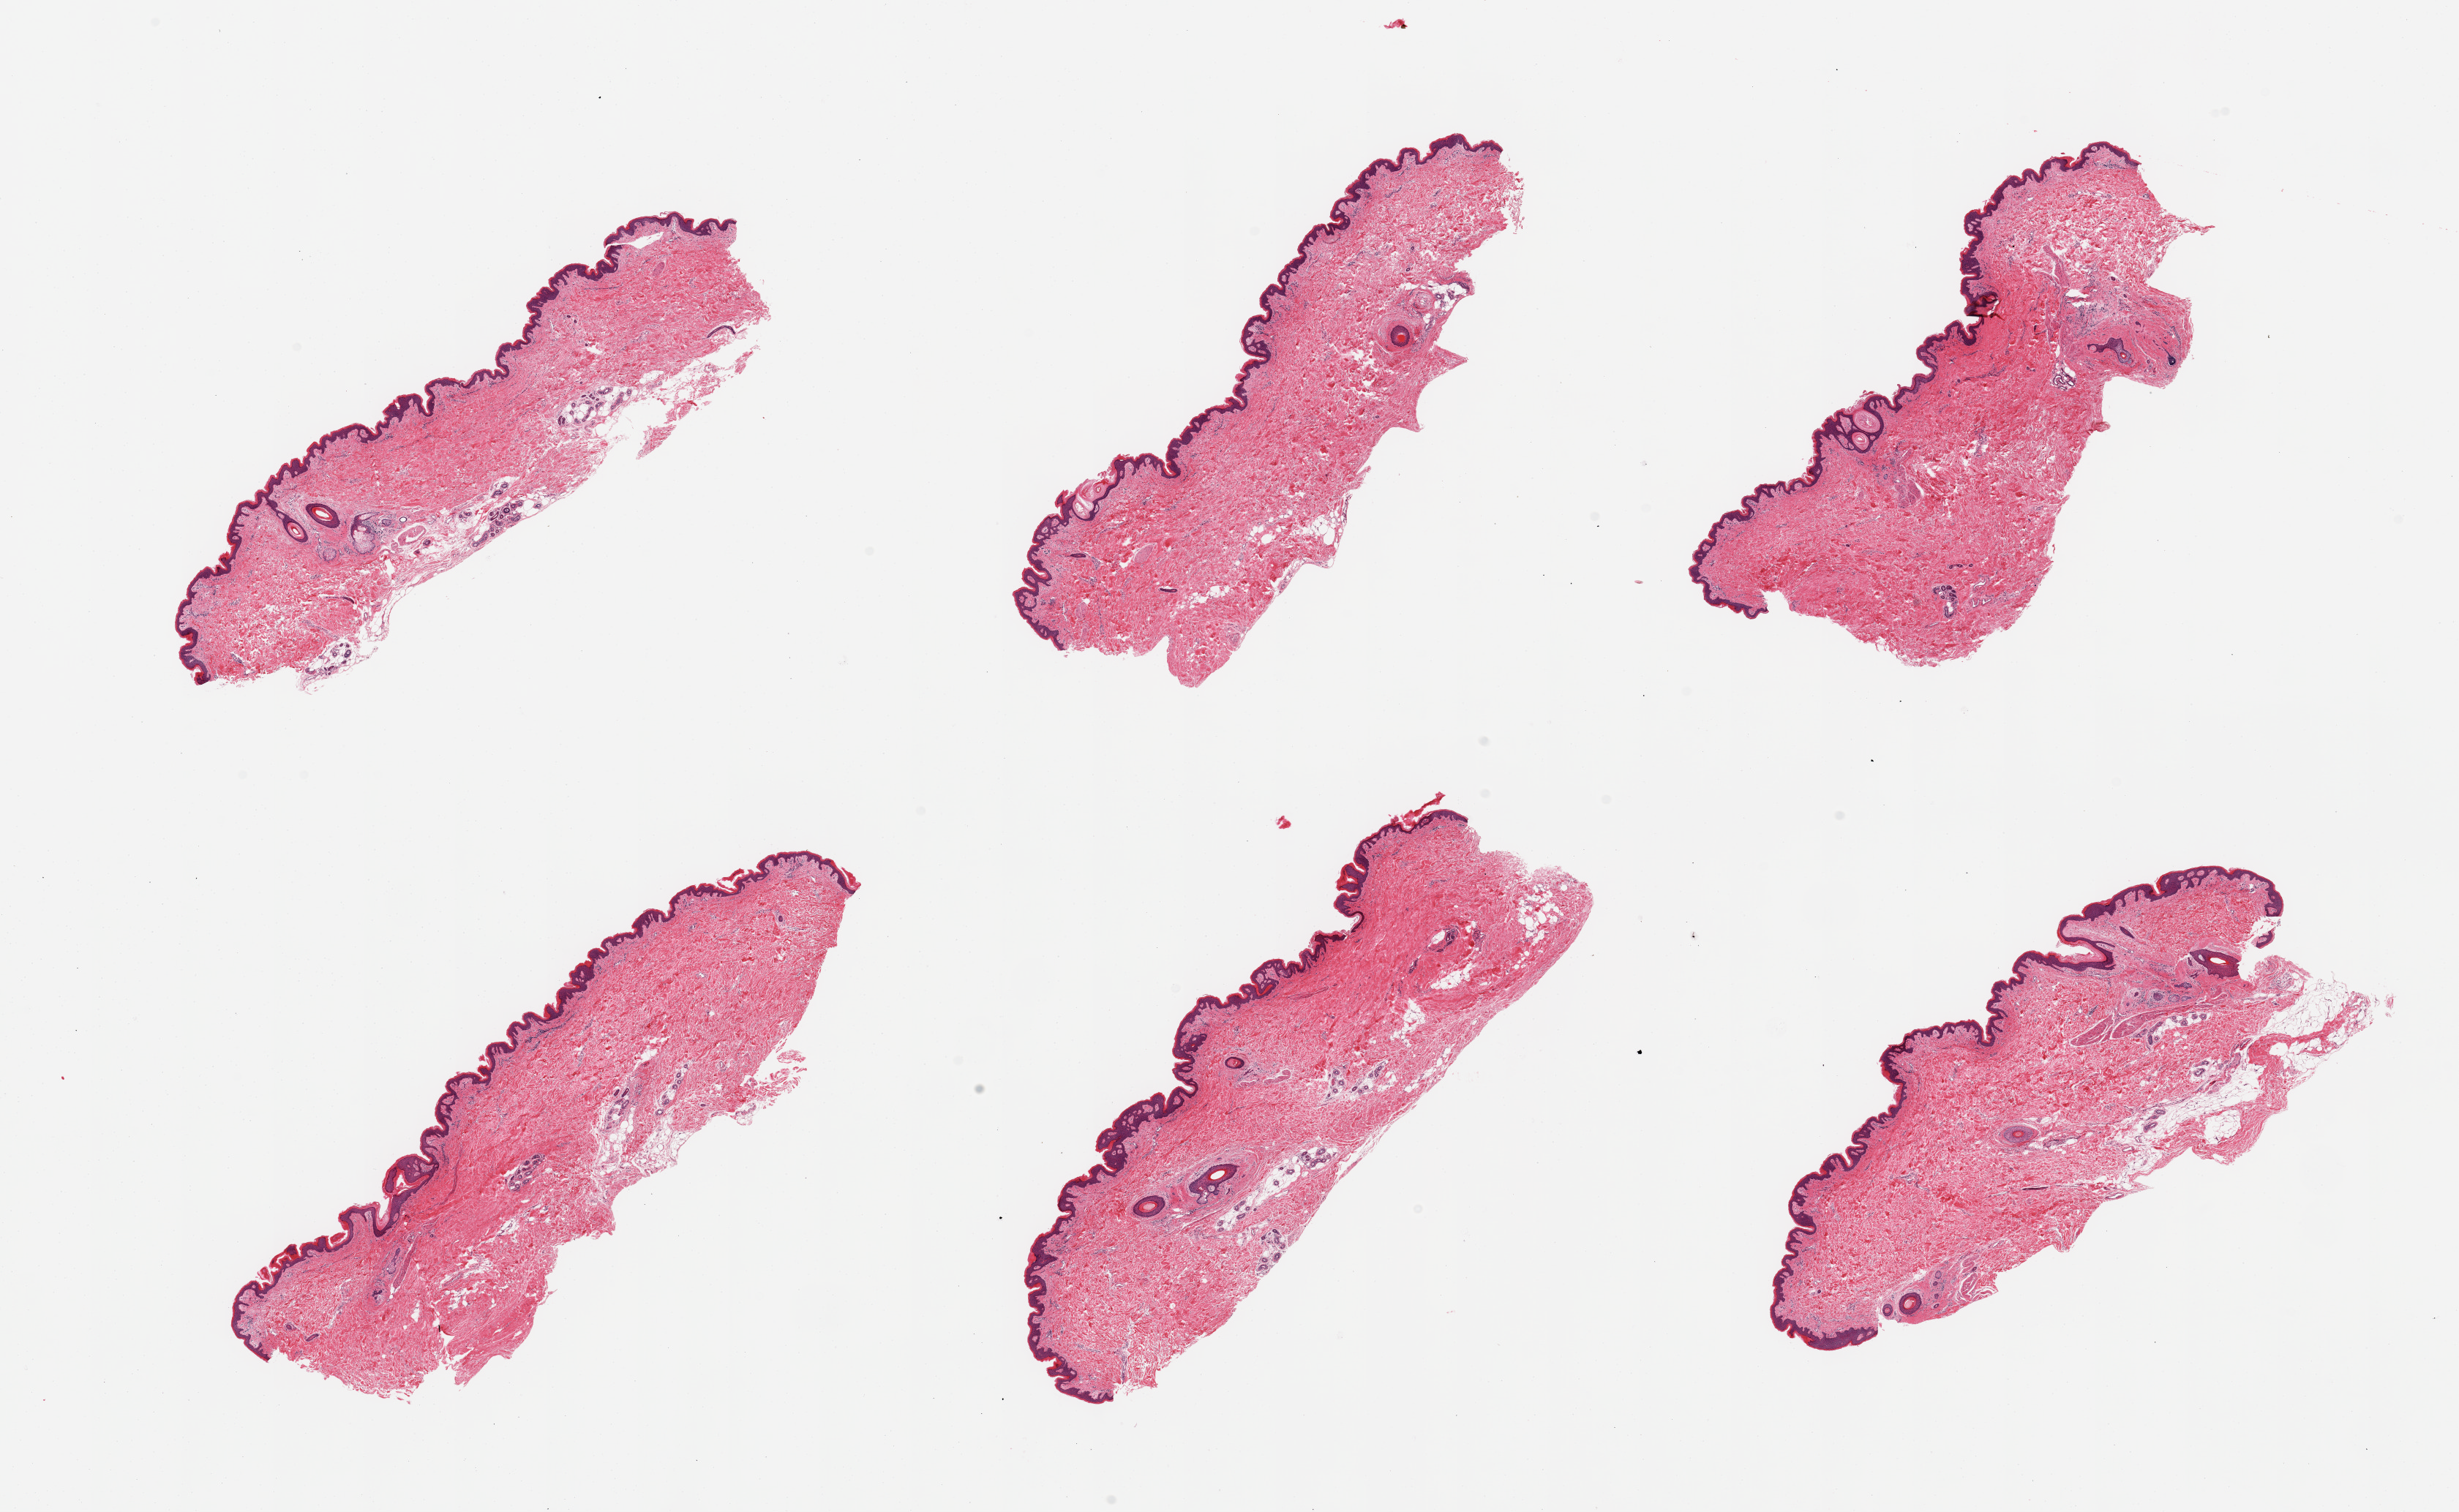
Whole-slide image, haematoxylin and eosin stain, brightfield — whole scanned area (about 26.6 x 16.3 mm) shown as a low-resolution overview; PAXgene-fixed, paraffin-embedded tissue; target tissue: skin of suprapubic region; donor tissue sample. Donor: male.
• reviewer comment on this tissue sample: 6 pieces; relatively well trimmed, few pieces with ~10% internal fat